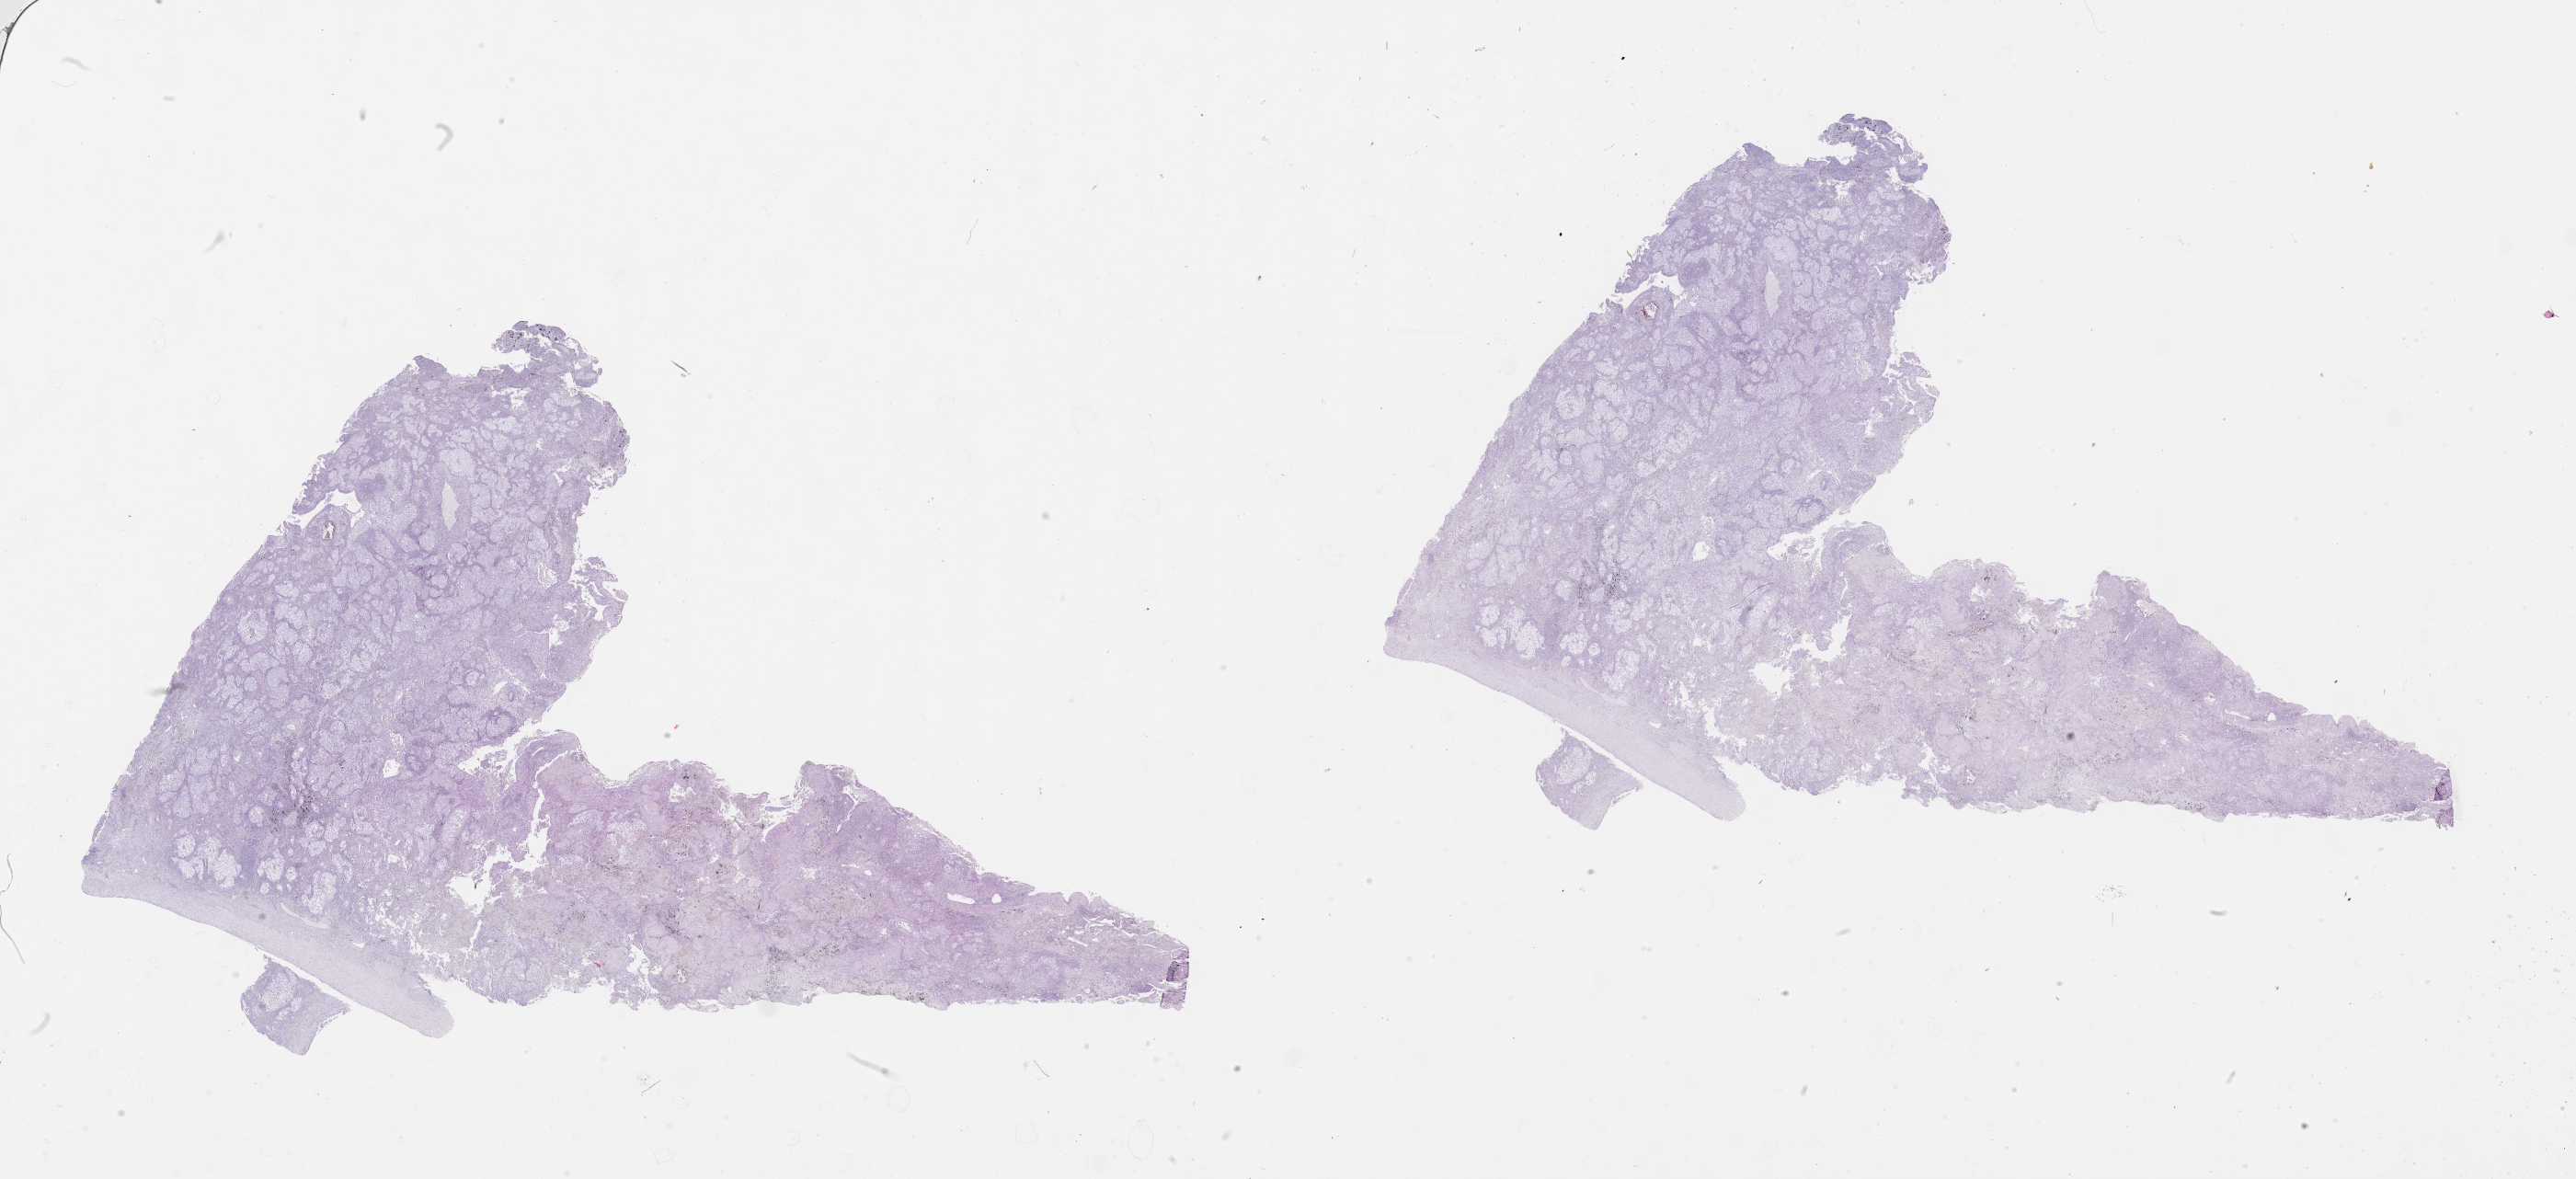
Digitized H&E-stained tissue section (whole slide), shown as a low-resolution overview of the whole scanned area (about 45.1 x 20.6 mm); tumour tissue sample, lung. Patient: male, age 68 years.
Patient diagnosis (cohort enrolment): squamous cell carcinoma (lung).